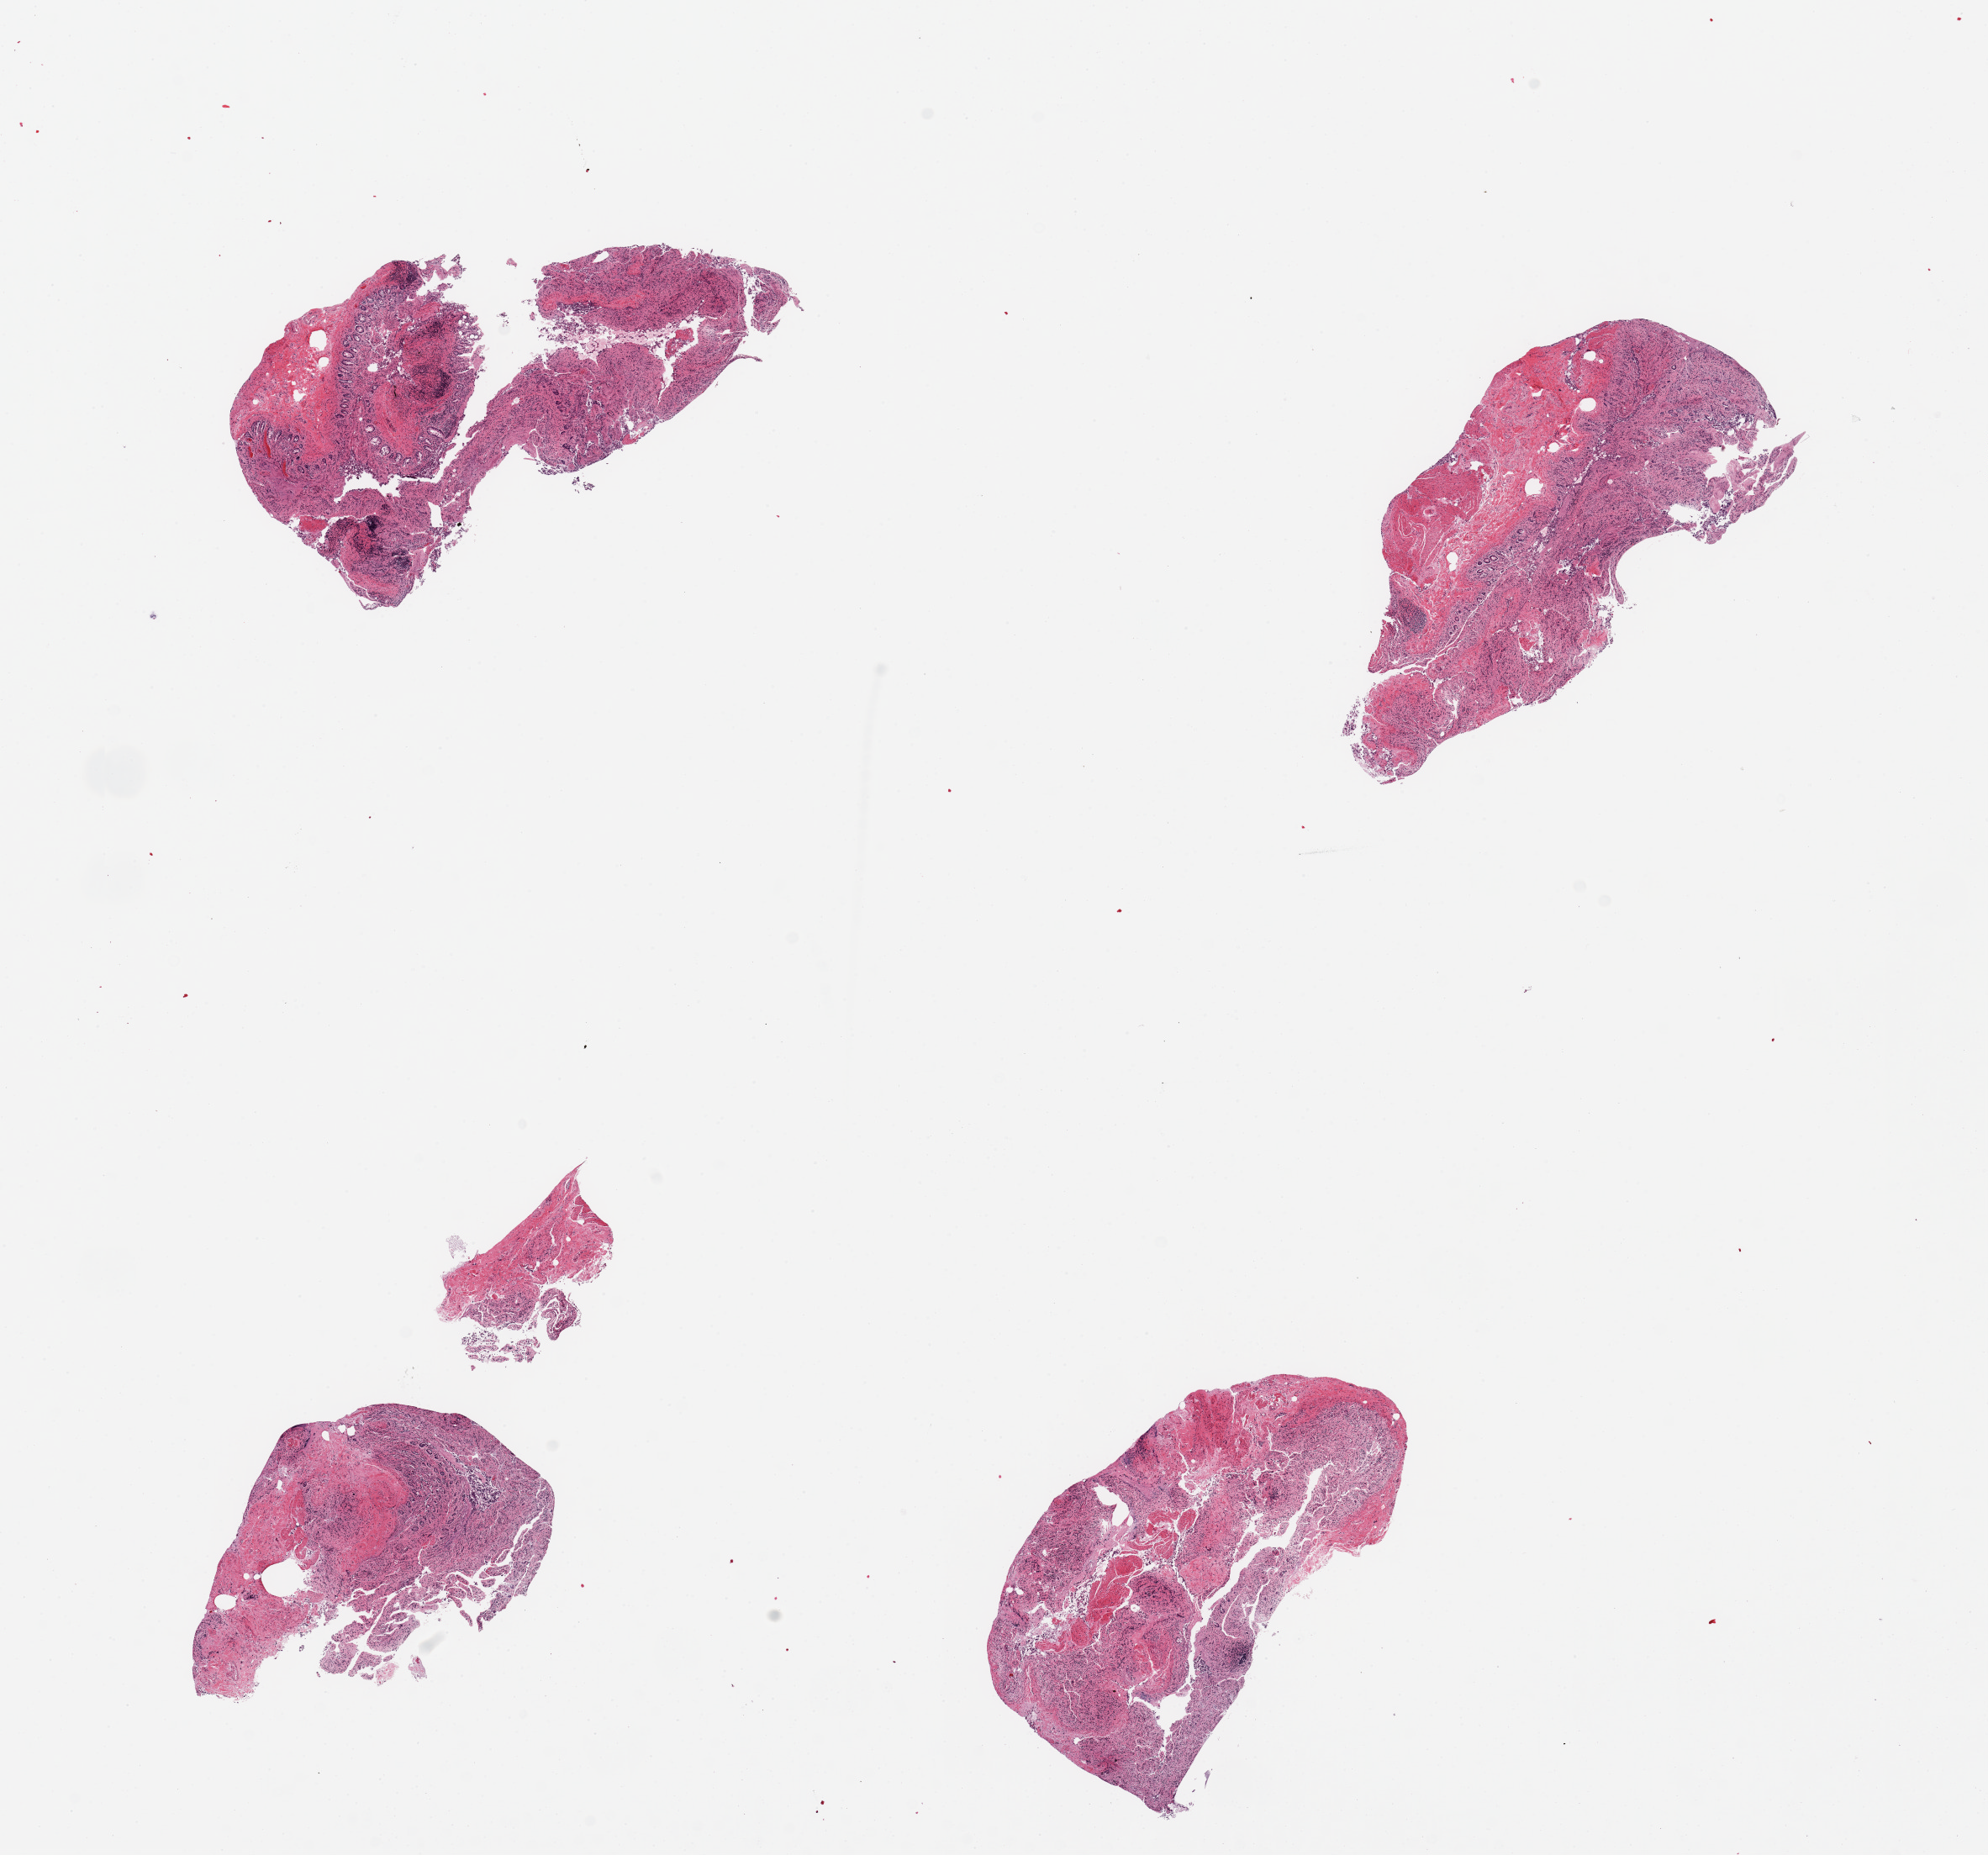
Hematoxylin and eosin (H&E) whole-slide image, brightfield, a low-resolution overview of the entire scanned area, about 18.7 x 17.5 mm. PAXgene-fixed paraffin-embedded (PFPE) section. Section of ileum (target tissue). Donor tissue sample. Female donor.
Pathologist's review note for this sample: 4 pieces, marked autolysis; ~15% lymphoid elements, largely dispersed.